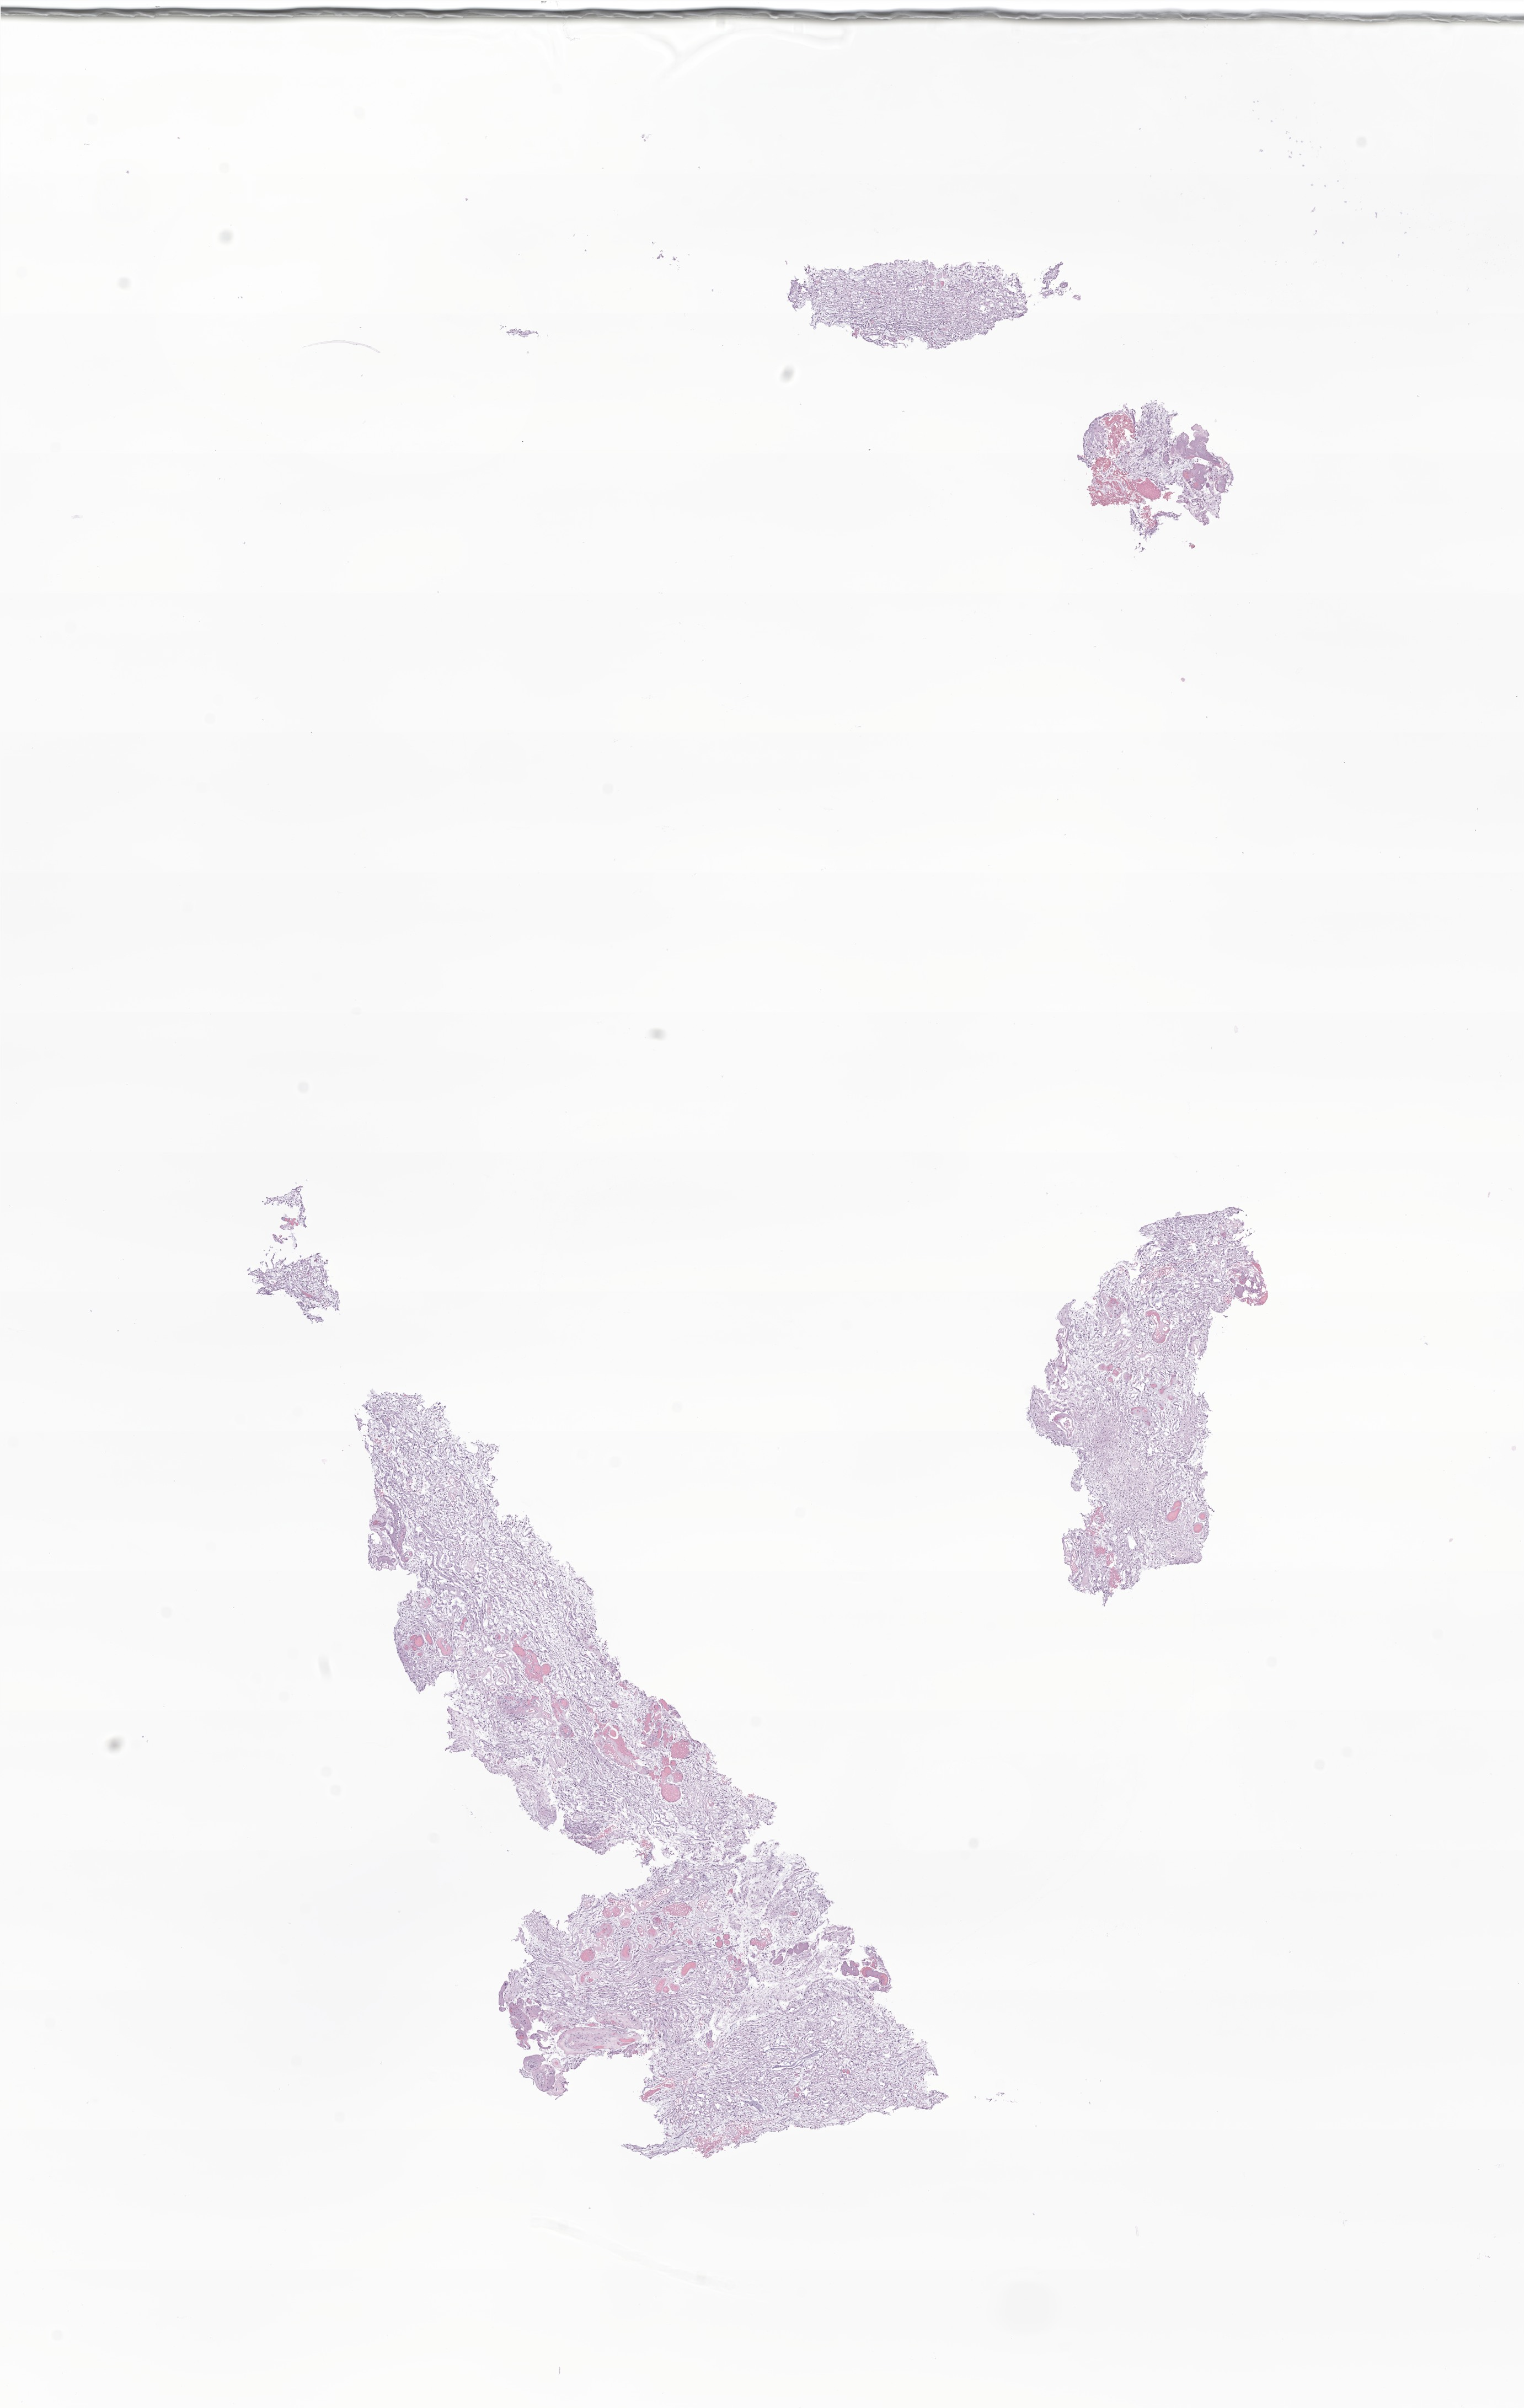
Haematoxylin and eosin whole-slide image of tumor tissue from the spinal cord — shown as a low-resolution overview of the whole scanned area (about 11.6 x 18.4 mm). FFPE section. Patient male; age 219 months.
* recorded diagnosis: Pilocytic astrocytoma